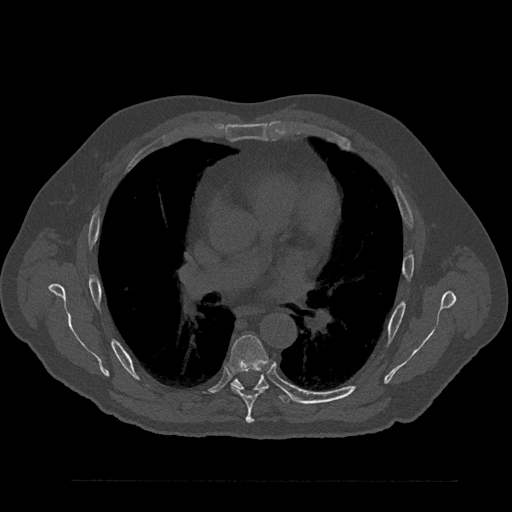
CT including the spine, one axial slice; position 536 of 797 along the scan axis; reconstruction kernel Br40s/3; 120 kVp; bone window (W 1800 / L 400 HU); 512 × 512 image matrix, field of view 430 × 430 mm. Patient: male, 61 years. From the clinical record (not read from this slice): primary cancer: prostate.
Outlined on this slice (semi-automatic segmentation, software-assisted and operator-edited):
- T6 vertebra: bounding box (x1, y1, x2, y2) in pixels: (228, 335, 270, 424)
- T7 vertebra: (232, 372, 291, 404)